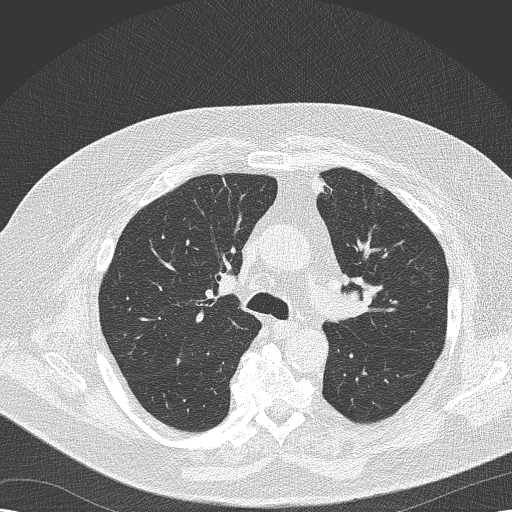
Axial slice from a low-dose chest CT screening exam. Second annual screen. Lung window (W 1500 / L -600 HU). Lung (sharp) reconstruction kernel (B50f). Slice 62 of 173 in the series. 512 × 512 image matrix. Male participant, aged 68 years at enrolment. Former smoker at enrolment.
Lesion marked by an expert reader, bounding box <323,269,374,334> (left, top, right, bottom; pixels). The exam's reader record, not a measurement of the box and not confirmed to be the same lesion: non-calcified nodule or mass ≥4 mm, left lower lobe, 8 × 6 mm, soft tissue attenuation, pre-existing on the prior screen: yes; interval growth: no. Later outcome: lung cancer diagnosed 256 days after this screen — squamous cell carcinoma, NOS, left upper lobe, poorly differentiated (G3), stage IIB (AJCC 6th edition), 35 mm at pathology.